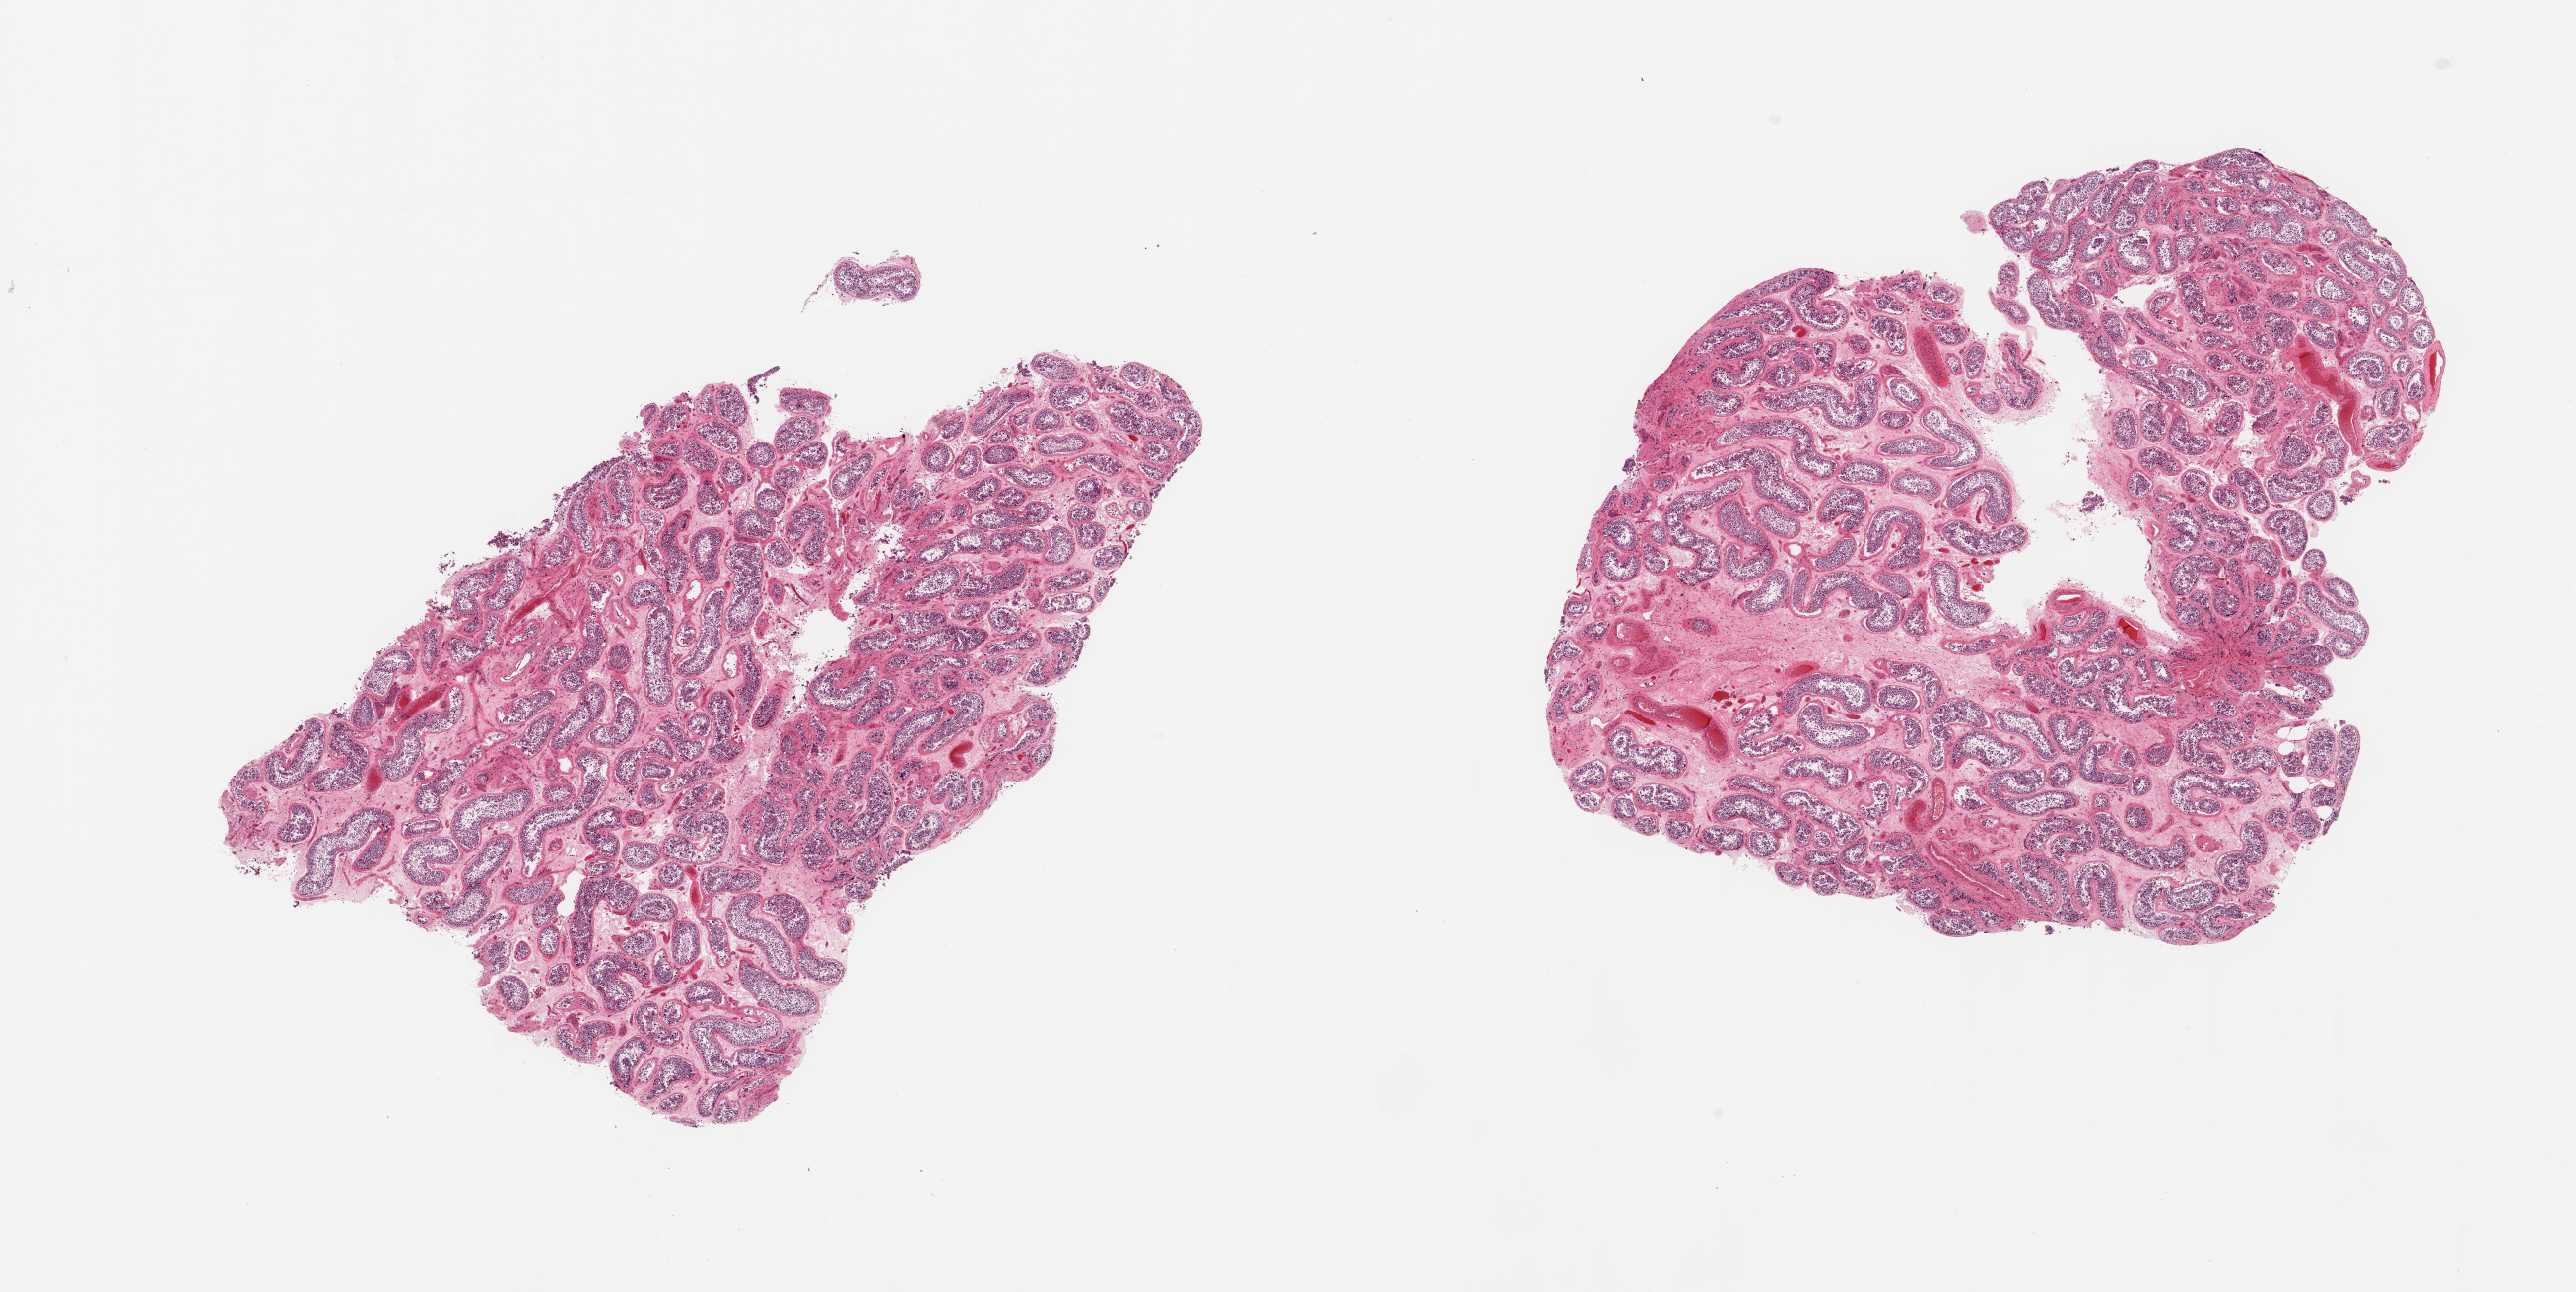
Whole-slide image, hematoxylin and eosin (H&E) stain, brightfield — a low-resolution overview of the entire scanned area, about 20.7 x 10.4 mm. PAXgene-fixed, paraffin-embedded tissue. Target tissue: testis. Donor tissue sample. Male donor.
Review note (as recorded): 2 pieces, moderate interstitial atrophy, reduced spermatogenesis.